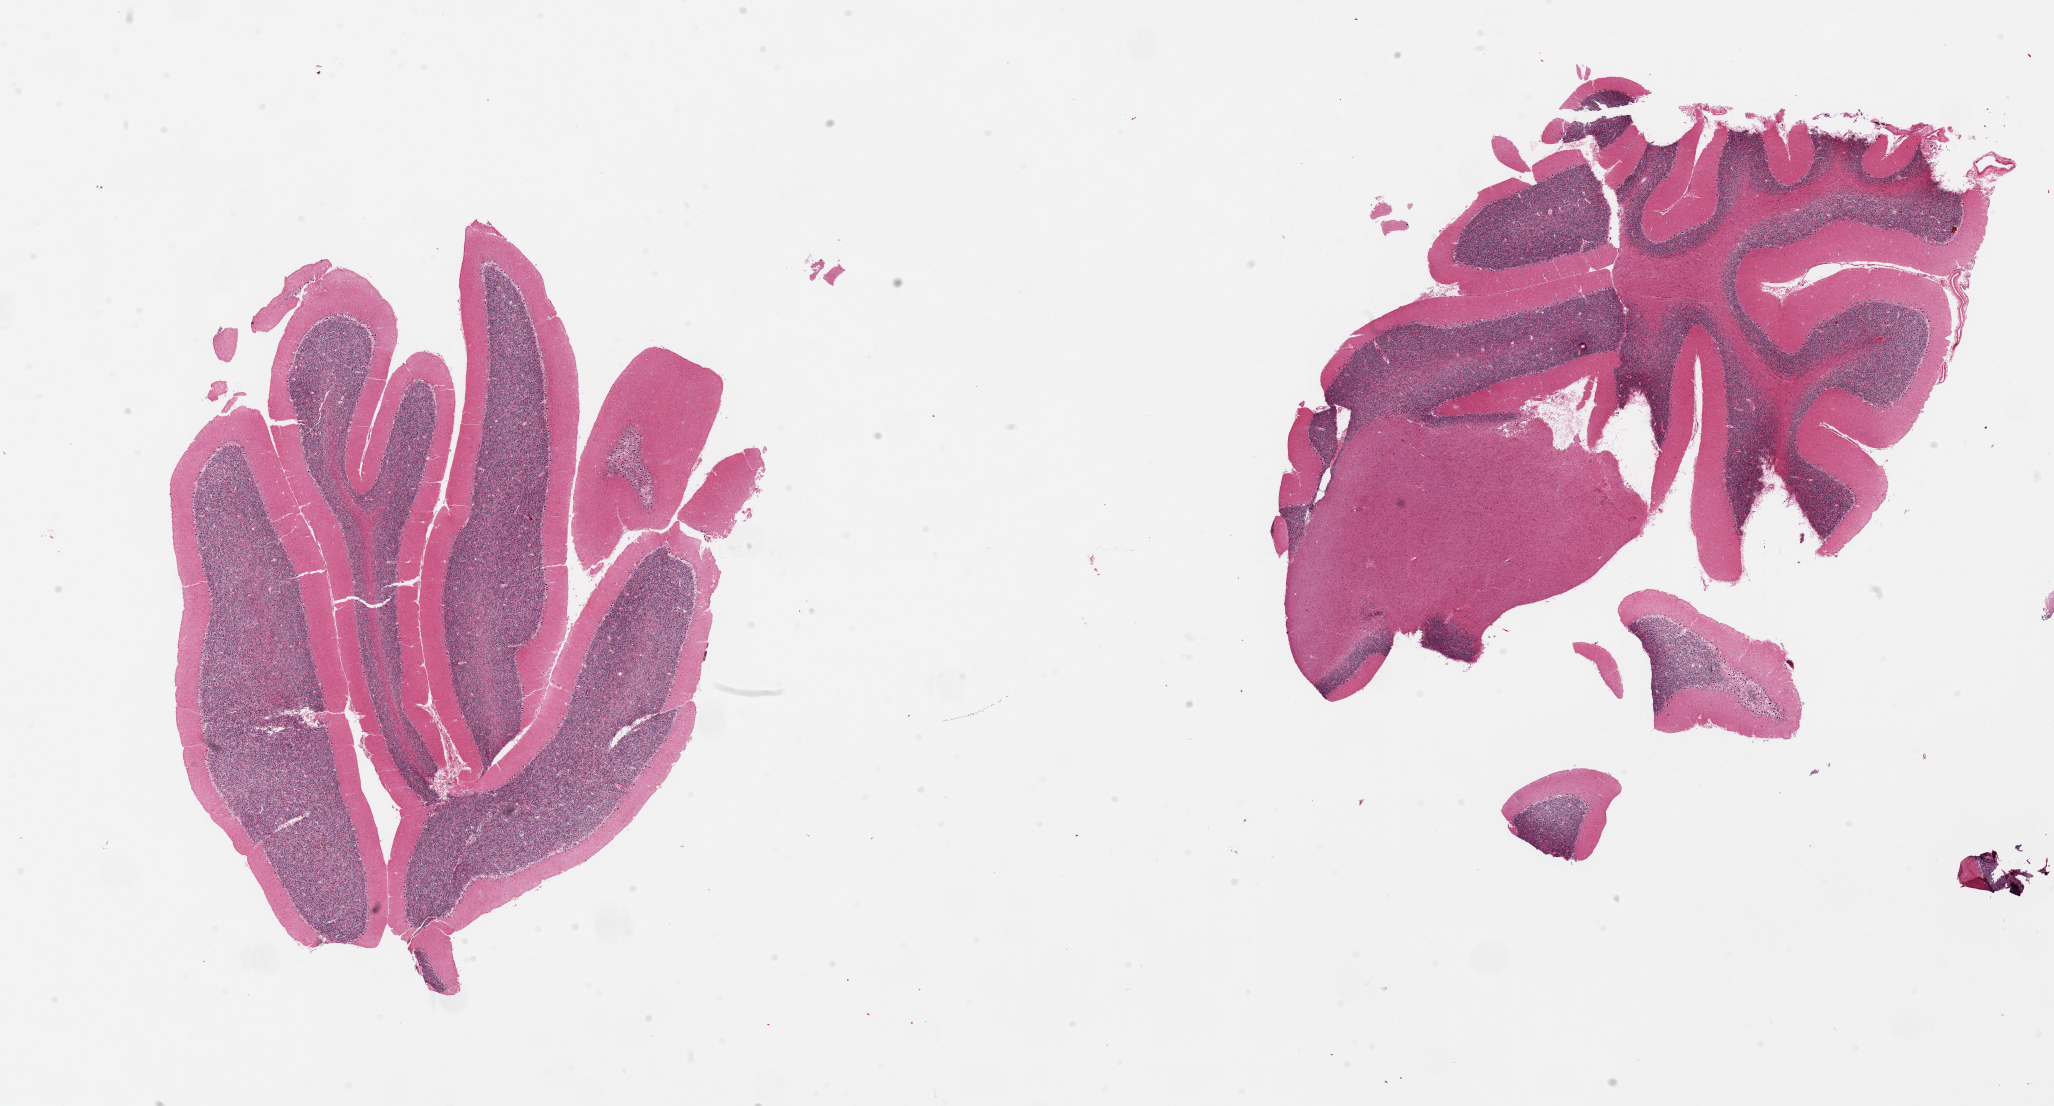
Digitized H&E-stained section, brightfield — a low-resolution overview of the entire scanned area, about 32.5 x 17.5 mm, PAXgene-fixed paraffin-embedded (PFPE) section, target tissue: cerebellum, donor tissue sample. Male donor.
Pathologist's review note for this sample: 2 pieces, no abnormalities.